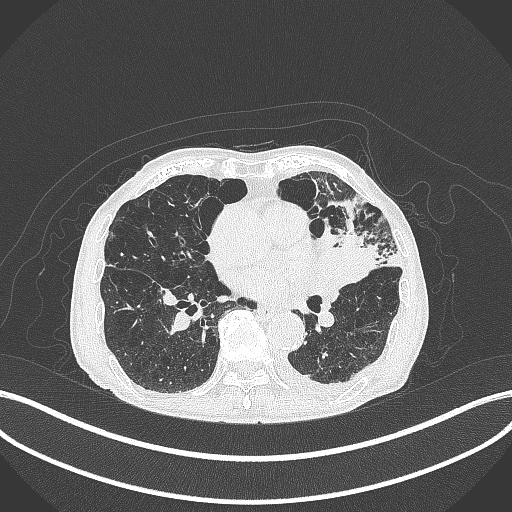
Chest CT, one axial slice. Slice 176 of 385 in the series (ordered by position). 120 kVp. Lung window (W 1500 / L -600 HU). 1 mm slice thickness. 512 × 512 image matrix, field of view 400 × 400 mm. Patient: male, 90 years or older. From the clinical record (not read from this slice): clinical TNM (as recorded): T2b N1 M0.
Outlined on this slice (rectangle marked by the reading radiologist):
- lung tumour (recorded histology: squamous cell carcinoma): bounding box [x1, y1, x2, y2] px = [312, 235, 383, 289]